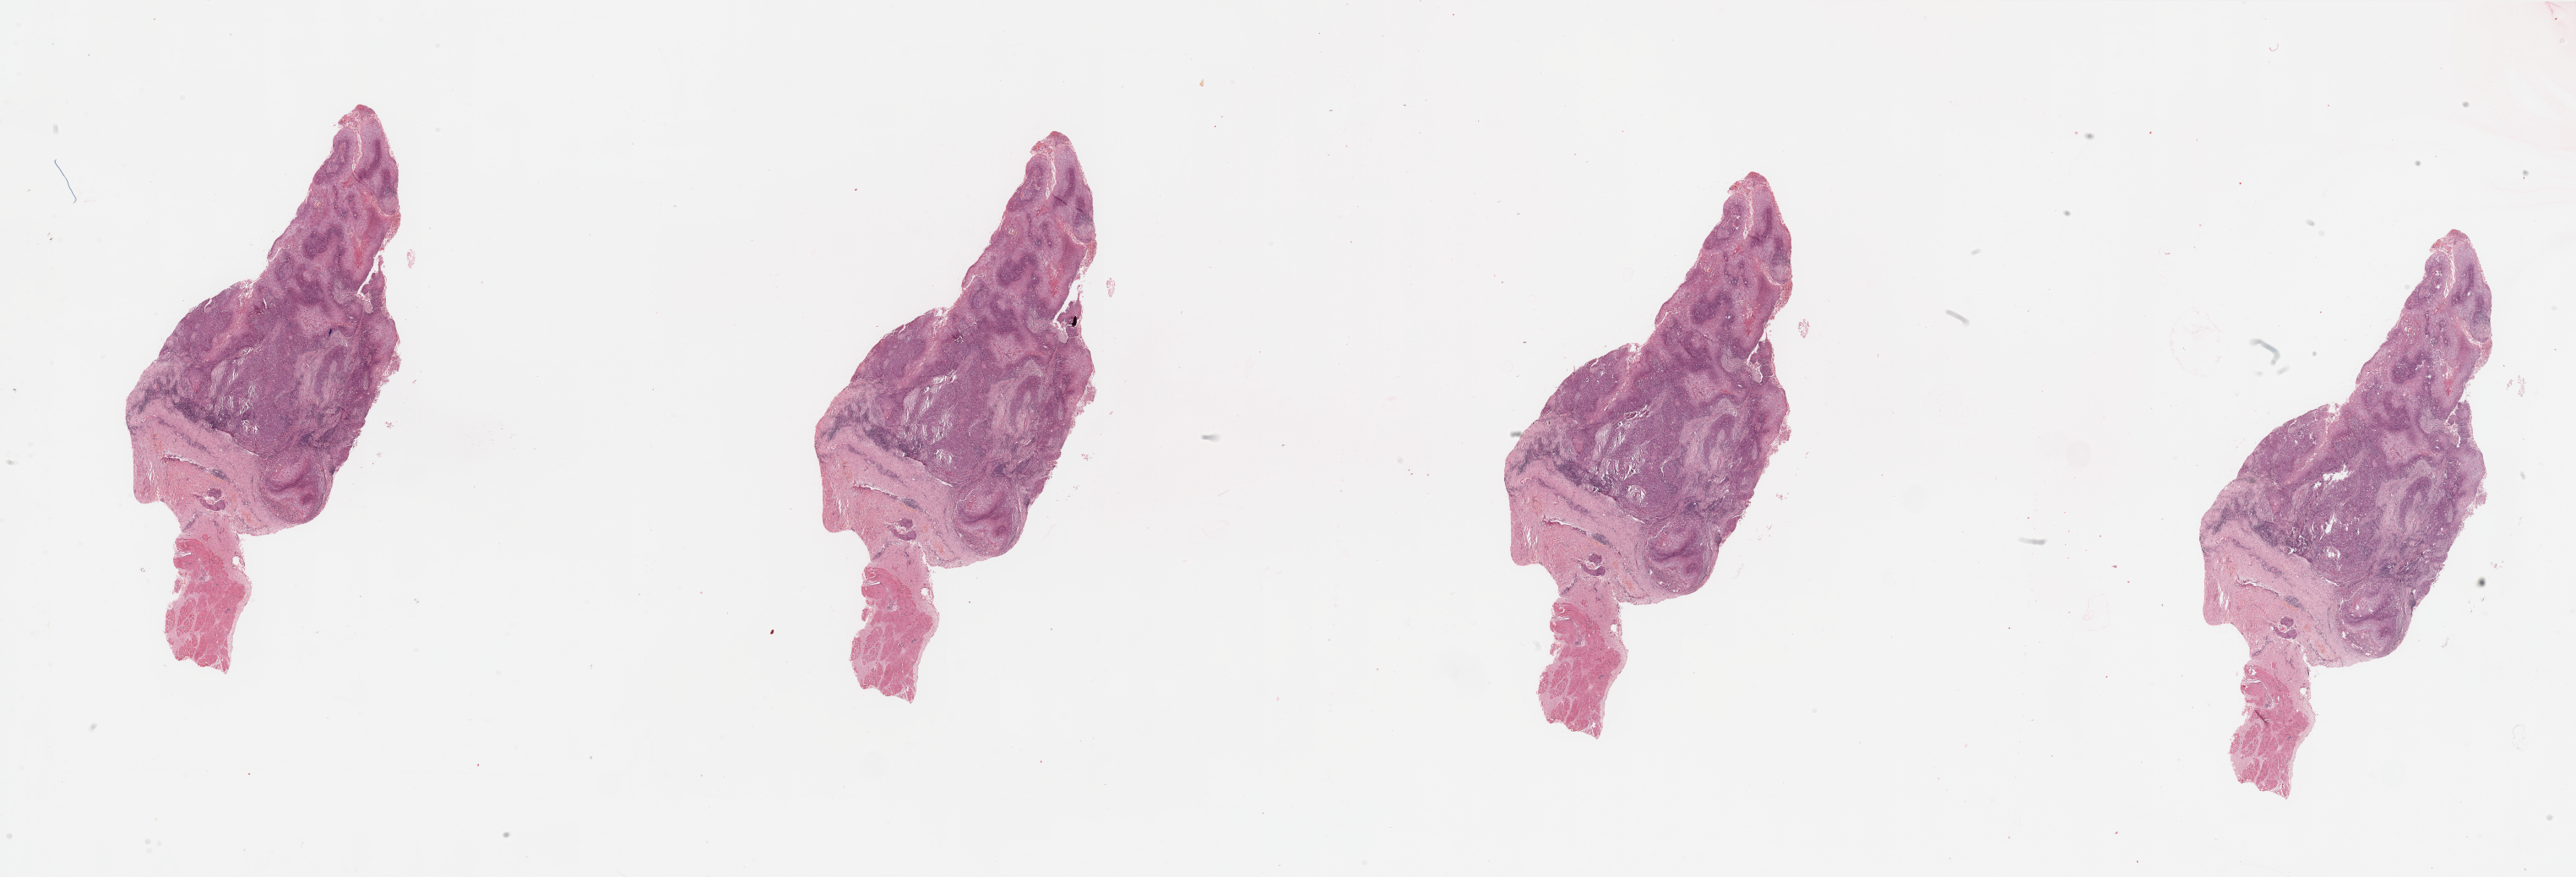
H&E-stained whole-slide image, whole scanned area (about 48.2 x 16.4 mm, acquisition: 20x scan) shown as a low-resolution overview; tumour tissue sample, sampled site: larynx. Male, 81 y/o. Histologic grade: G2 (moderately differentiated). Composition of this section per pathologist review: tumour nuclei 80%, necrosis 5%.
Diagnosis: Squamous cell carcinoma, NOS (larynx, NOS). AJCC pathologic stage: II. Primary tumour site (as recorded): larynx.